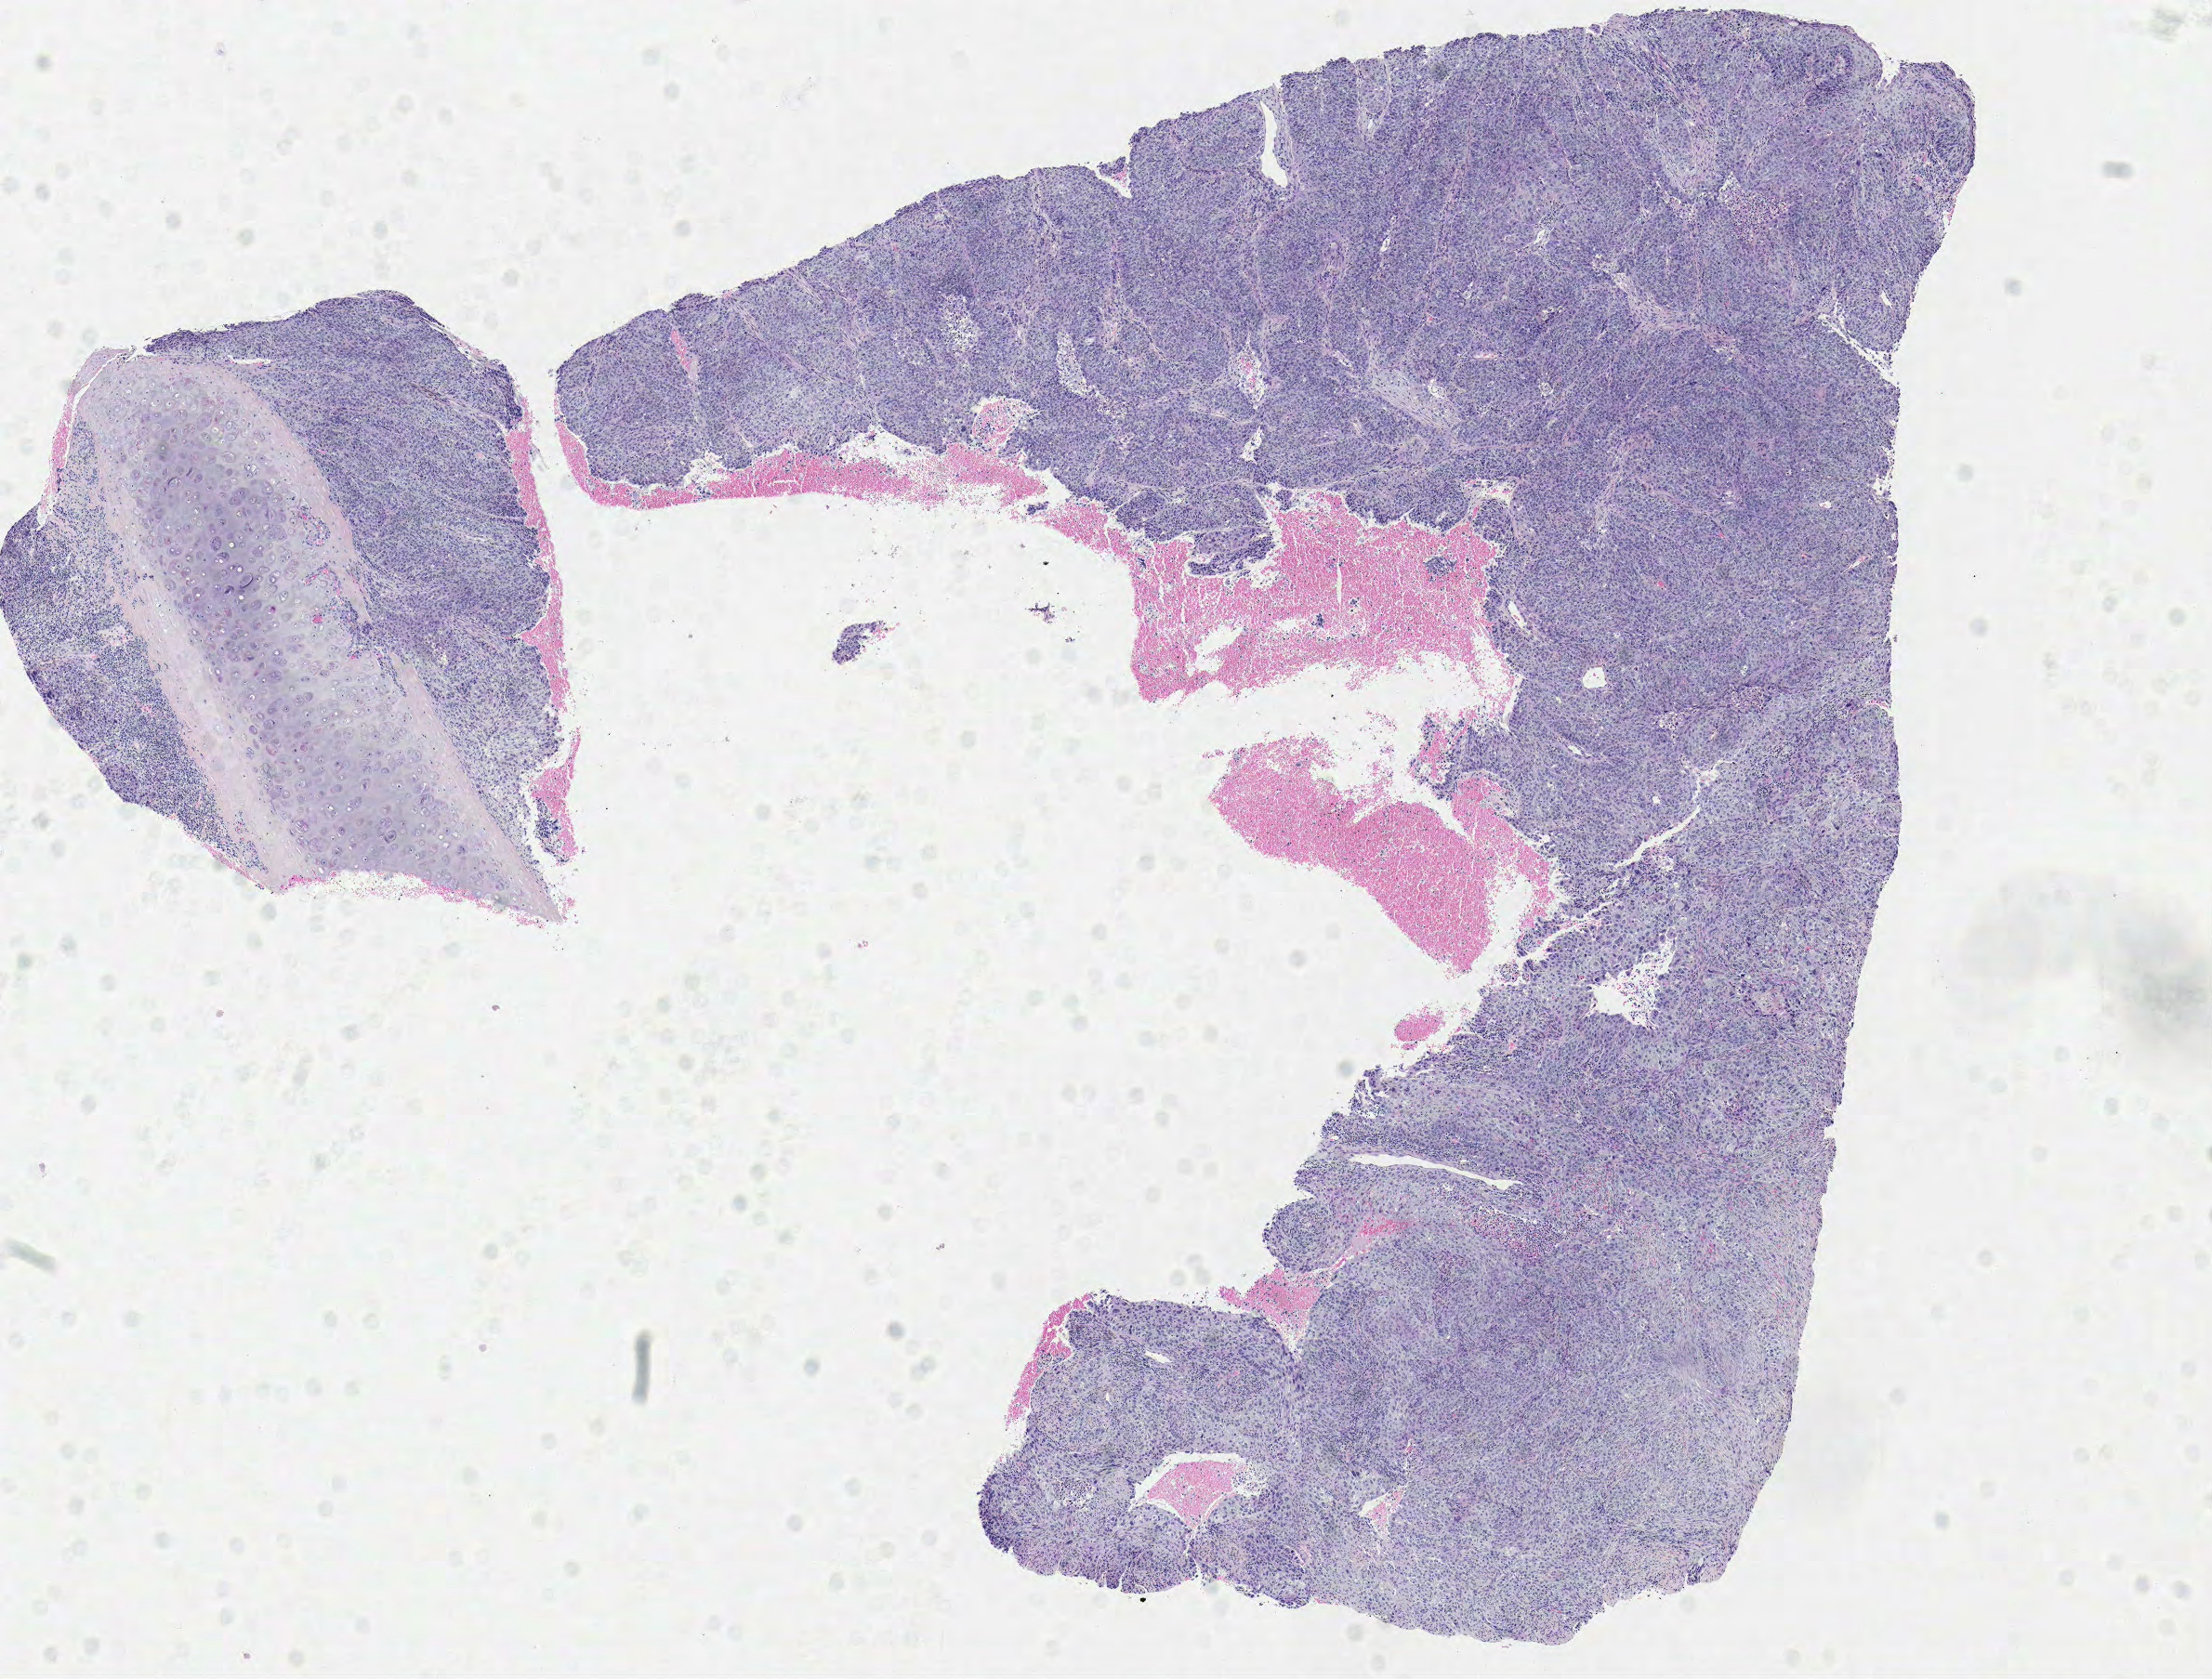
H&E whole-slide image — shown as a low-resolution overview of the whole scanned area (about 9.4 x 7.1 mm), formalin-fixed paraffin-embedded (FFPE) diagnostic section, lung, primary tumour sample. Male, age 72 years at initial diagnosis.
* TNM: T2 N1 M0
* laterality: left
* pathologic diagnosis: Squamous cell carcinoma, NOS
* AJCC pathologic stage: IIB (6th edition)